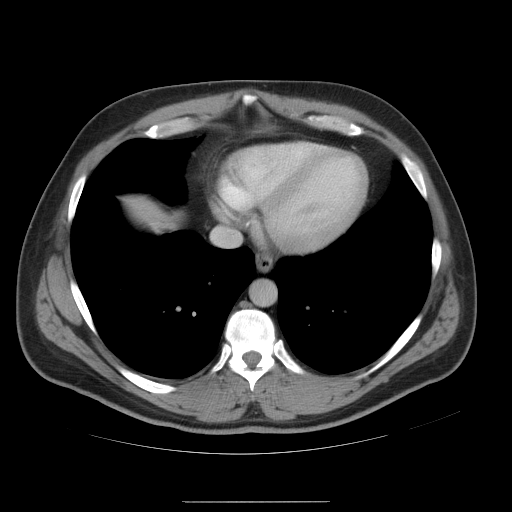
Contrast-enhanced abdominal CT, one axial slice. Position 49 of 54 along the scan axis. 120 kVp. Intravenous contrast given. Soft-tissue window (W 400 / L 40 HU). 5 mm slice thickness. 512 × 512 image matrix. Male patient, age 40 years. From the clinical record (not read from this slice): diagnosis: colorectal cancer liver metastases, imaged before liver resection; multiple liver metastases: no; largest metastasis: 15 cm; disease in both lobes: no.
Outlined on this slice (manually delineated by an expert):
- hepatic veins: bounding box (x1, y1, x2, y2) in pixels: (213, 234, 217, 238)
- liver: (123, 195, 185, 233)